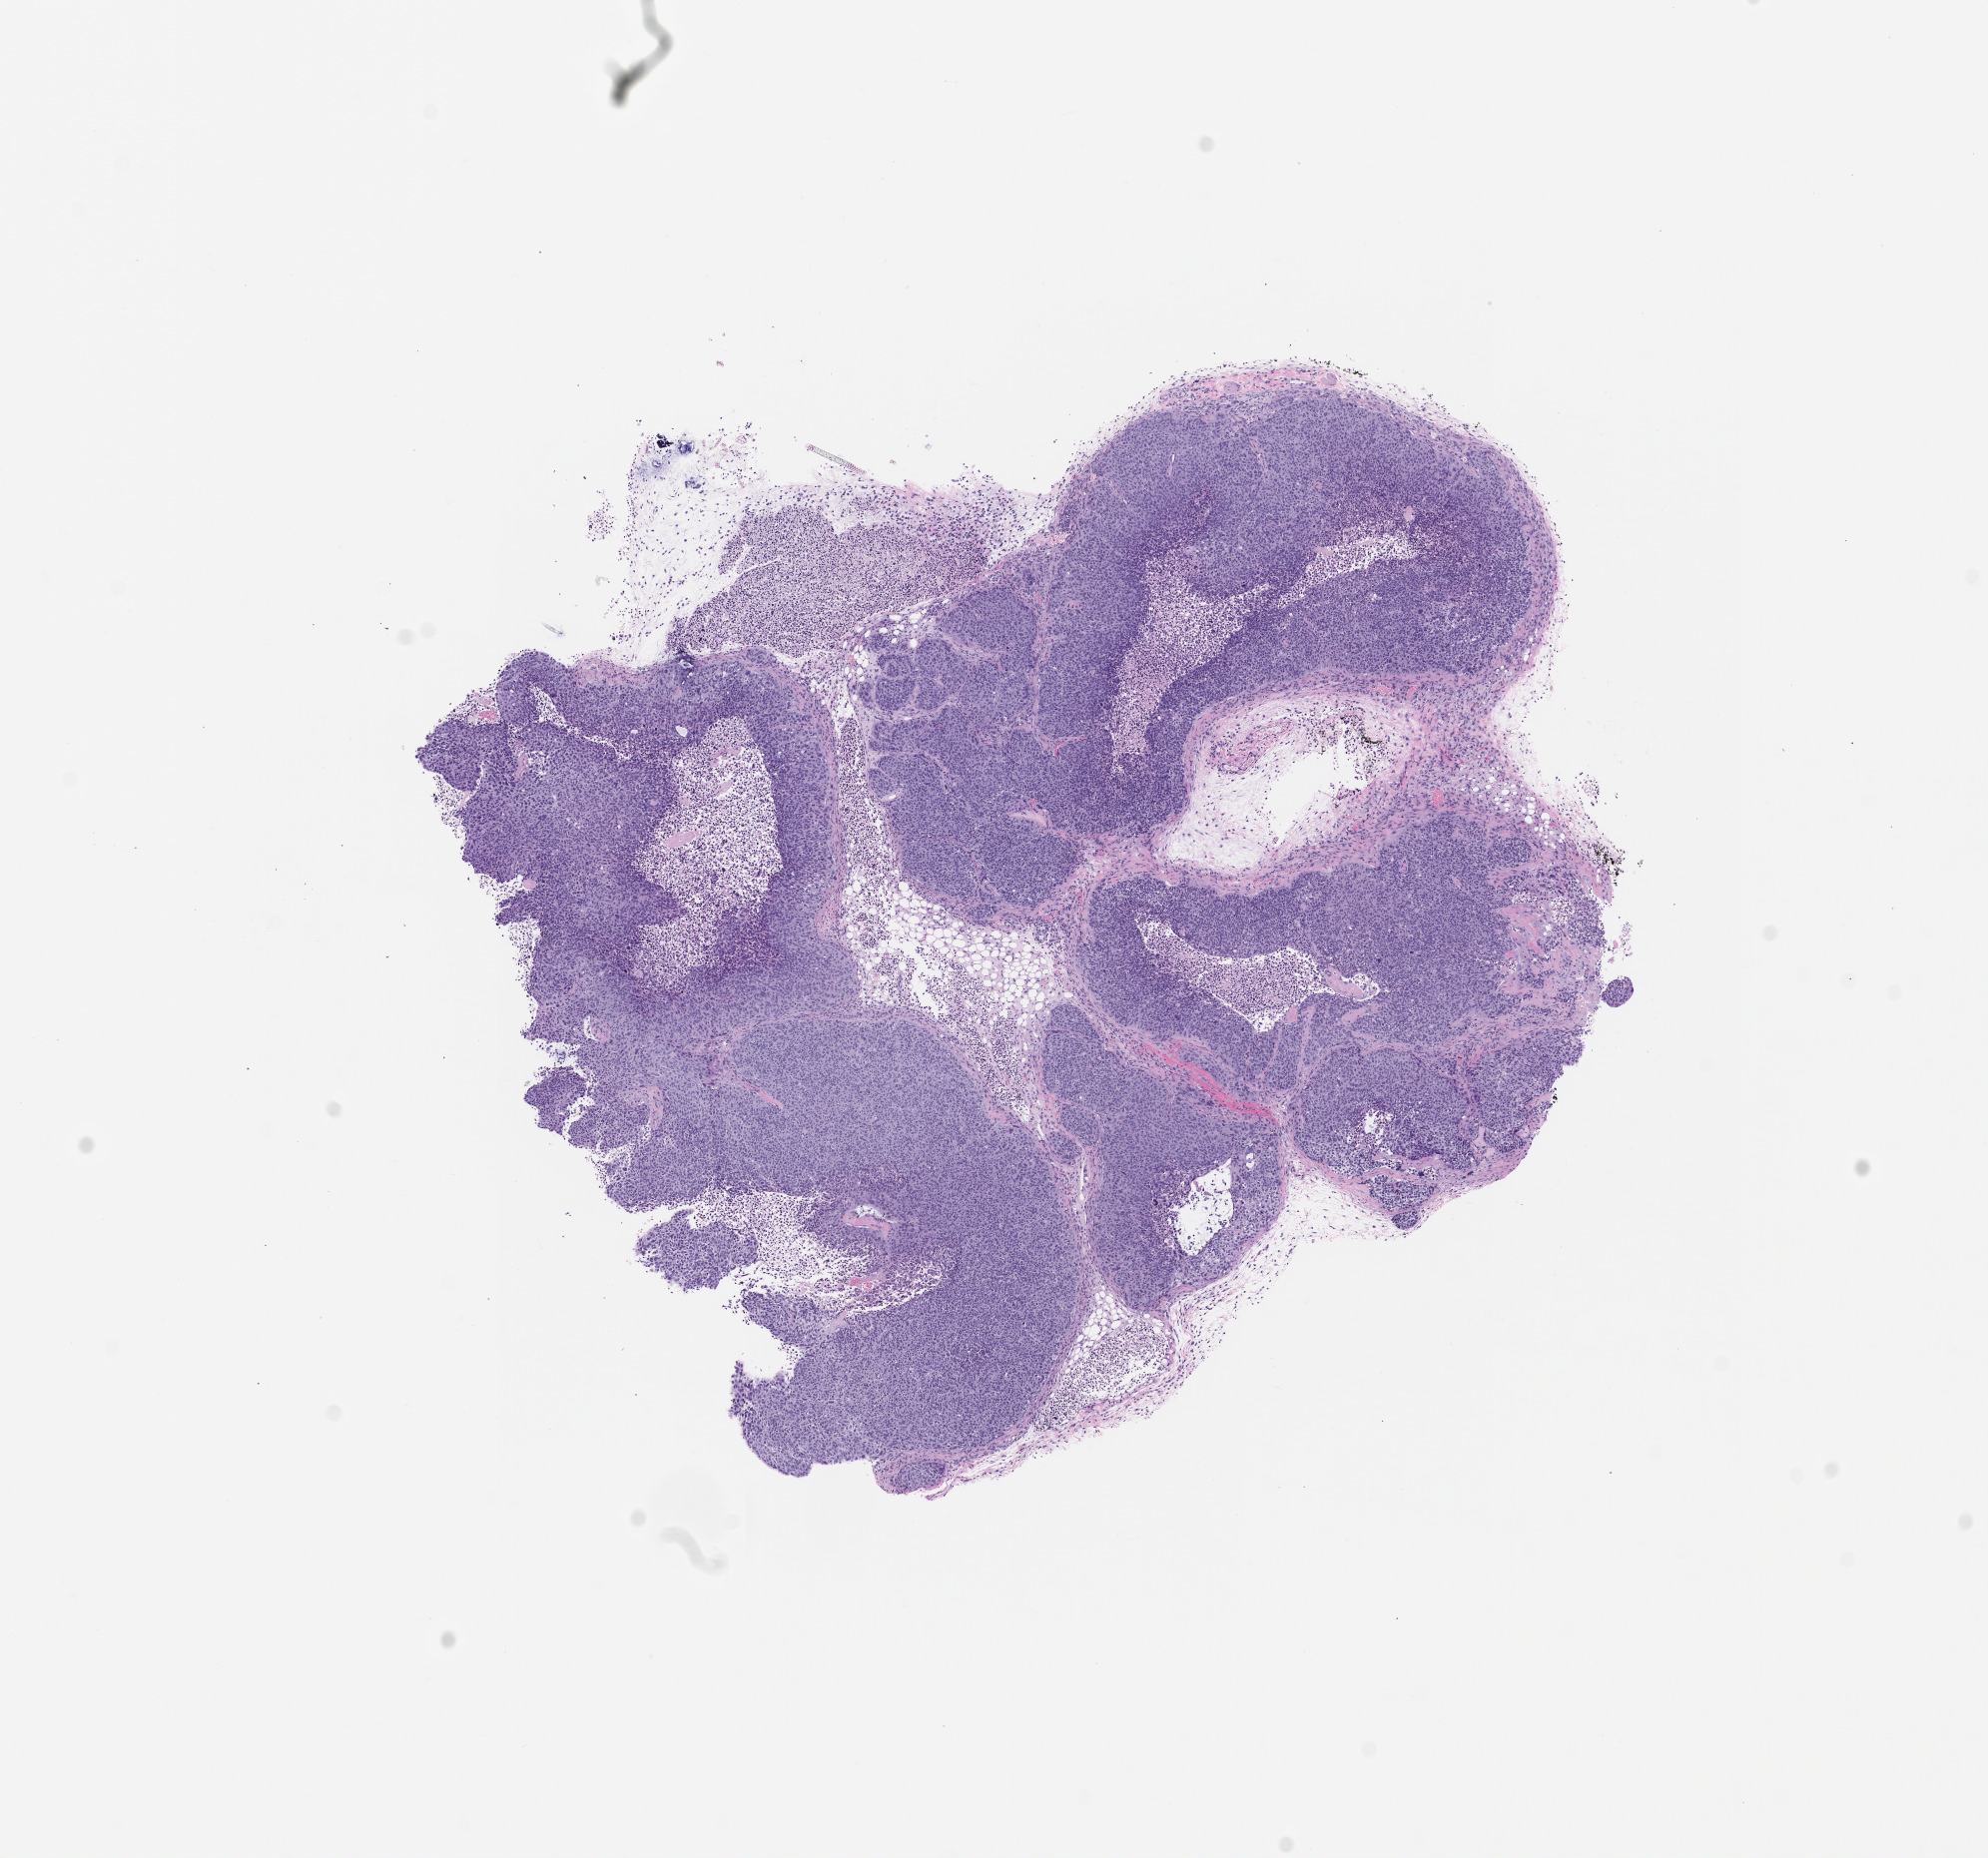
Hematoxylin and eosin (H&E) whole-slide image of a patient-derived xenograft (PDX) tumor grown in a mouse, passage 0, a low-resolution overview of the entire scanned area, about 8.0 x 7.5 mm. FFPE section. Tumor site category: head and neck.
- originating patient diagnosis: Head and Neck Squamous Cell Carcinoma